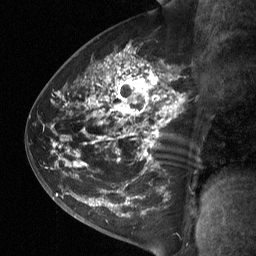
Breast MRI (dynamic contrast-enhanced), one sagittal slice; position 38 of 64 along the scan axis; dynamic contrast-enhanced study with each time point stored as its own series, time point 2 of 3 at this slice position (early post-contrast, ordered by acquisition time); 1.5 T; TE 4.8 ms, TR 27 ms; 2 mm slice thickness; 256 × 256 image matrix. Patient: female, 42 years. From the clinical record (not read from this slice): setting: breast cancer imaged before/during neoadjuvant chemotherapy; receptor status: triple-negative.
Outlined on this slice (semi-automatically segmented with operator editing):
- analysis volume of interest (the breast-tissue region the enhancement analysis was run in; not a lesion): bounding box <49,45,193,197> (left, top, right, bottom; pixels)
- tumour enhancement mask (voxels above the 90 % enhancement threshold inside the analysis volume of interest): <66,54,178,166>